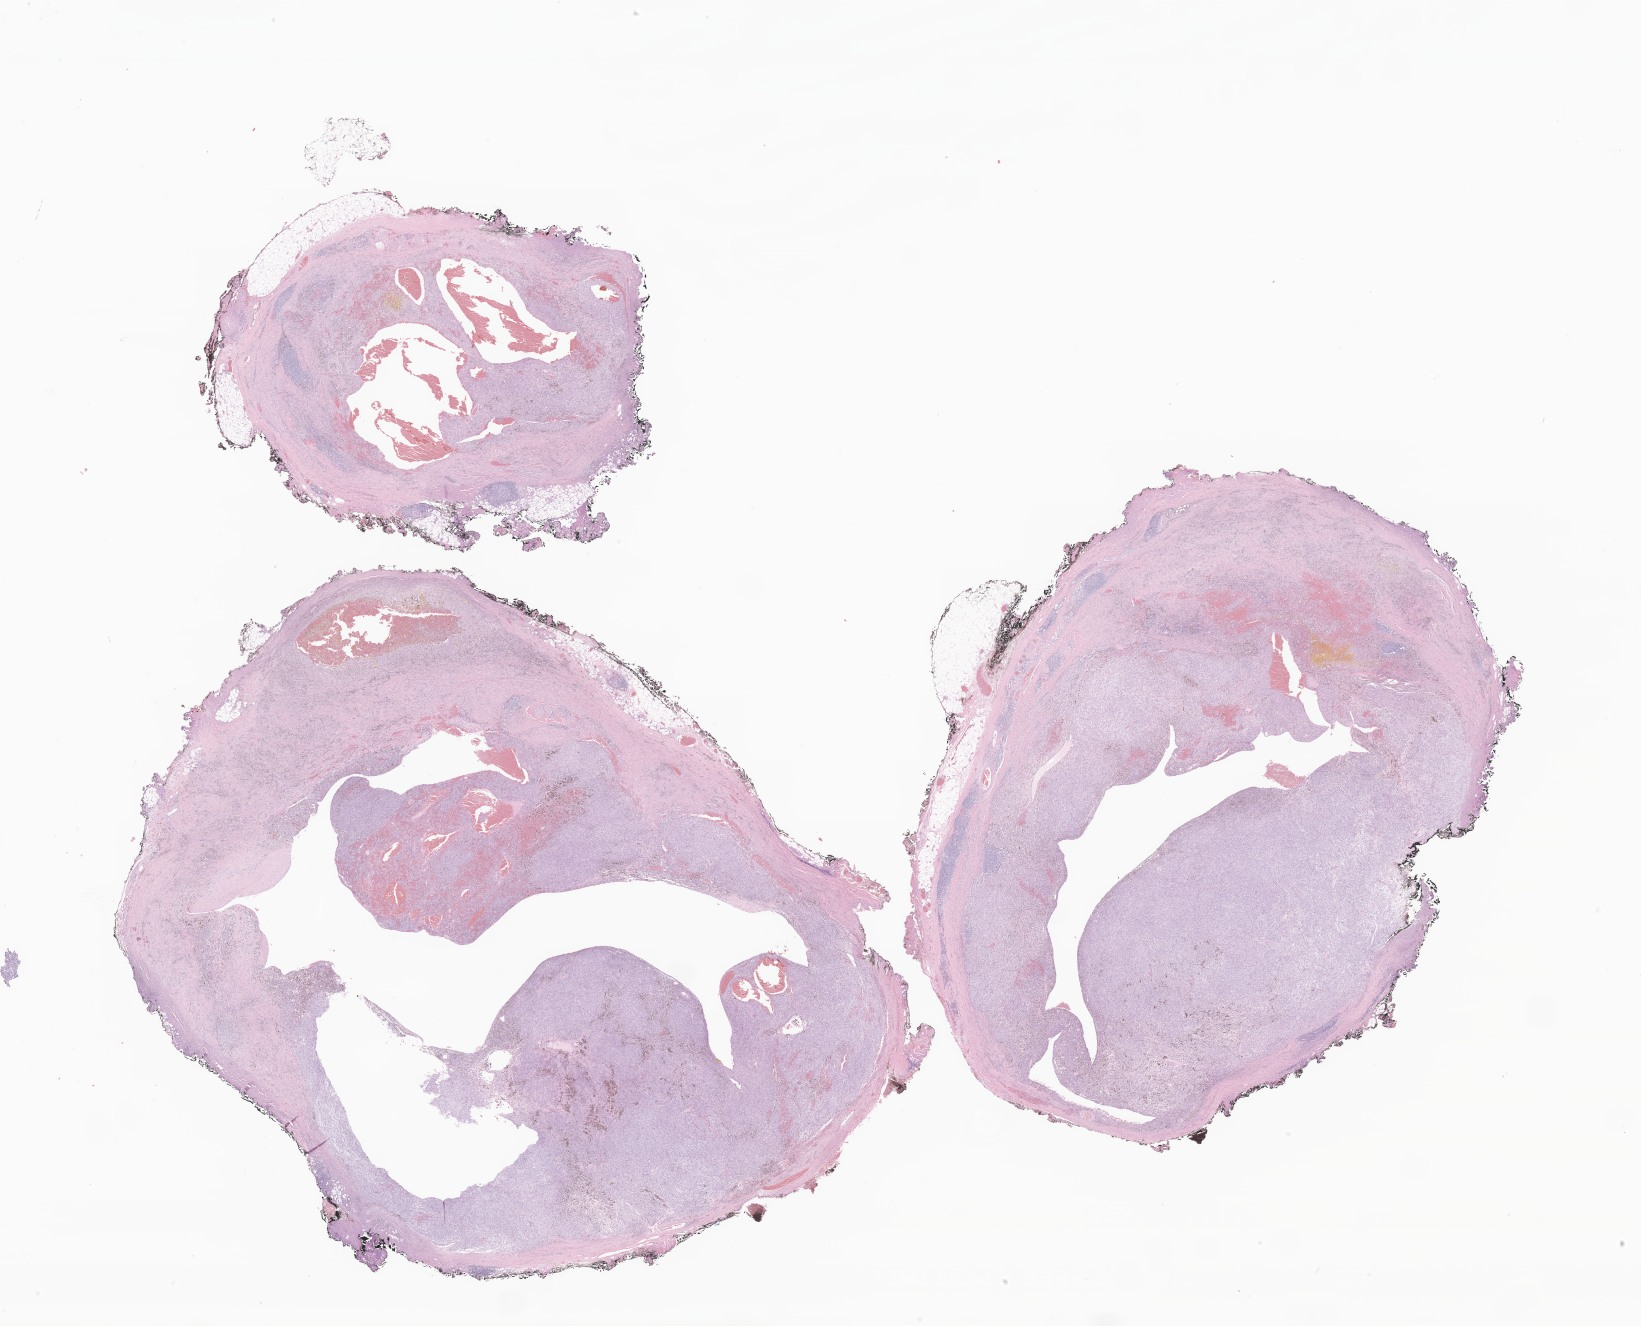
Digitized haematoxylin and eosin-stained section of tumor tissue from the upper limb lymph node, a low-resolution overview of the entire scanned area, about 27.7 x 22.4 mm. FFPE section. Patient male; age 90 months (7 years 6 months).
- diagnosis (ICD-O-3 morphology term): Angiomatoid fibrous histiocytoma